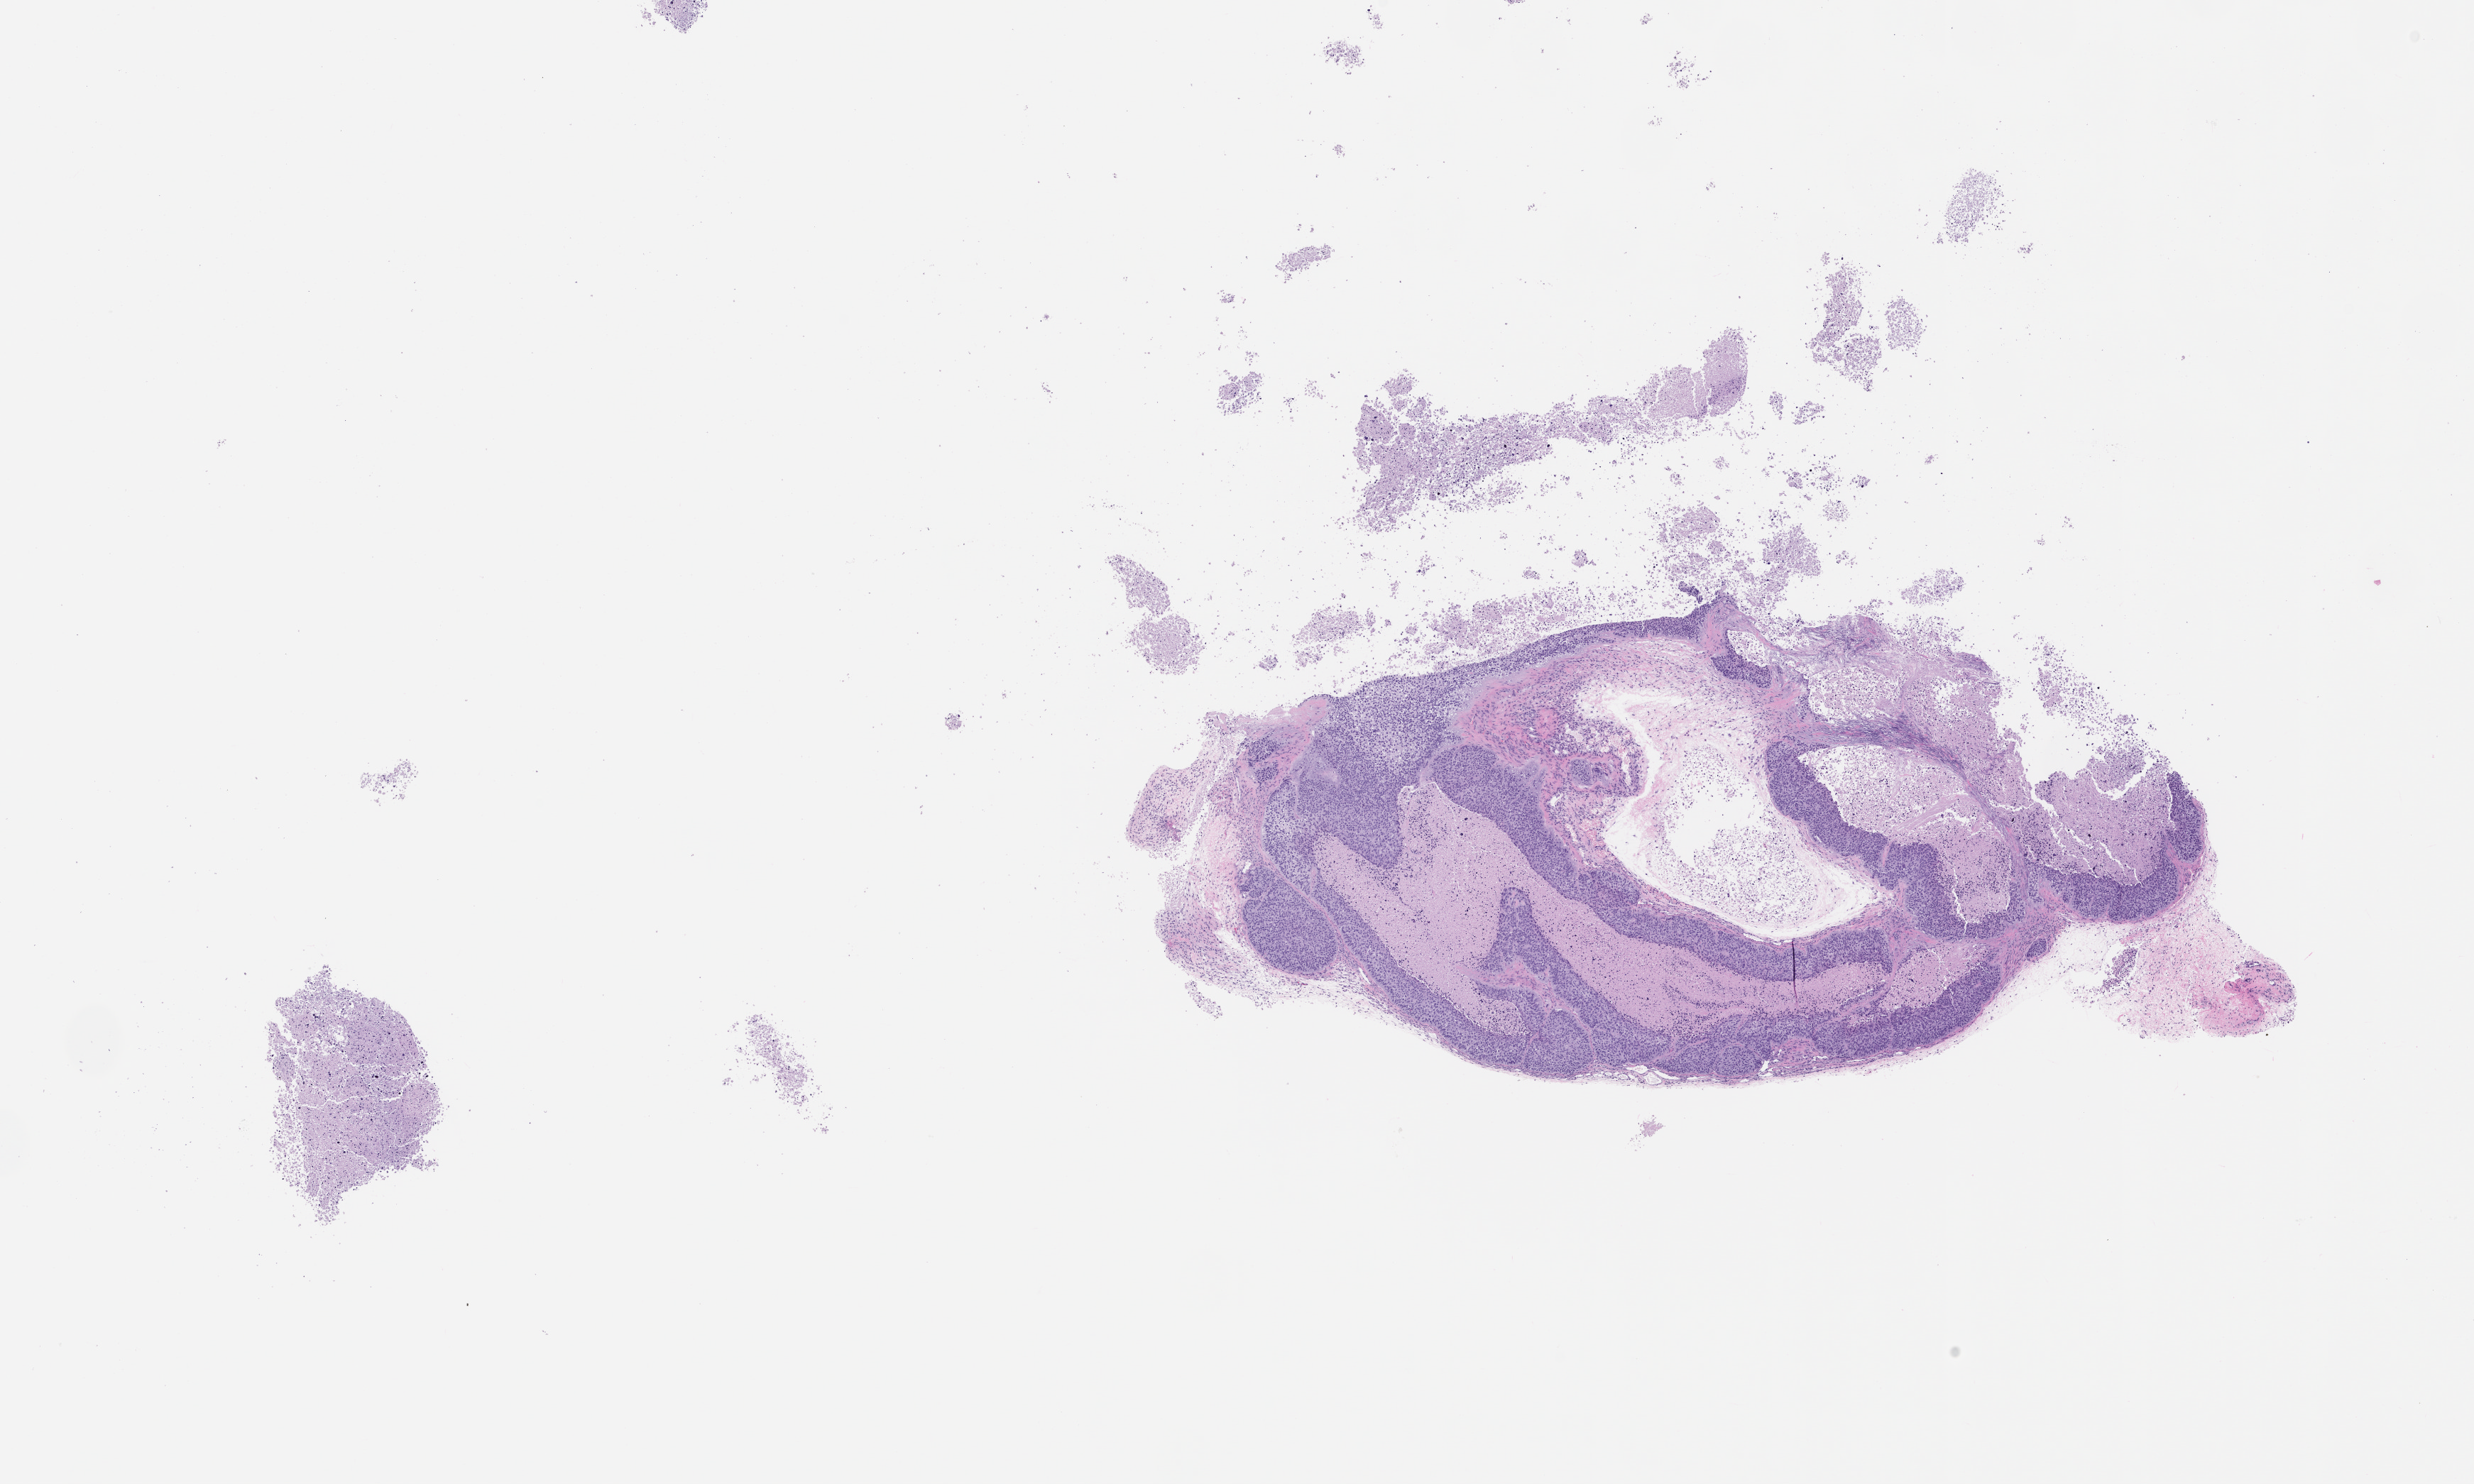
Hematoxylin and eosin (H&E) whole-slide image of a patient-derived xenograft (PDX) tumor grown in a mouse, passage 0 — whole scanned area (about 14.0 x 8.4 mm) shown as a low-resolution overview, formalin-fixed paraffin-embedded section, tumor site category: lung.
Originating patient diagnosis: Lung Squamous Cell Carcinoma.